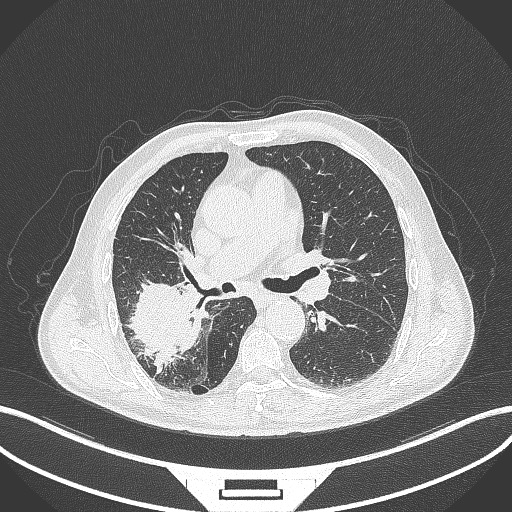
Chest CT, one axial slice; position 238 of 429 along the scan axis; reconstruction kernel B70f; lung window (W 1500 / L -600 HU); 1 mm slice thickness; 512 × 512 image matrix, field of view 400 × 400 mm. Patient: male, 72 years. From the clinical record (not read from this slice): clinical TNM (as recorded): T3 N2 M0.
Annotated regions visible in this slice (bounding box drawn by a radiologist):
- lung tumour (recorded histology: adenocarcinoma): box from (x=122, y=275) to (x=207, y=375) px